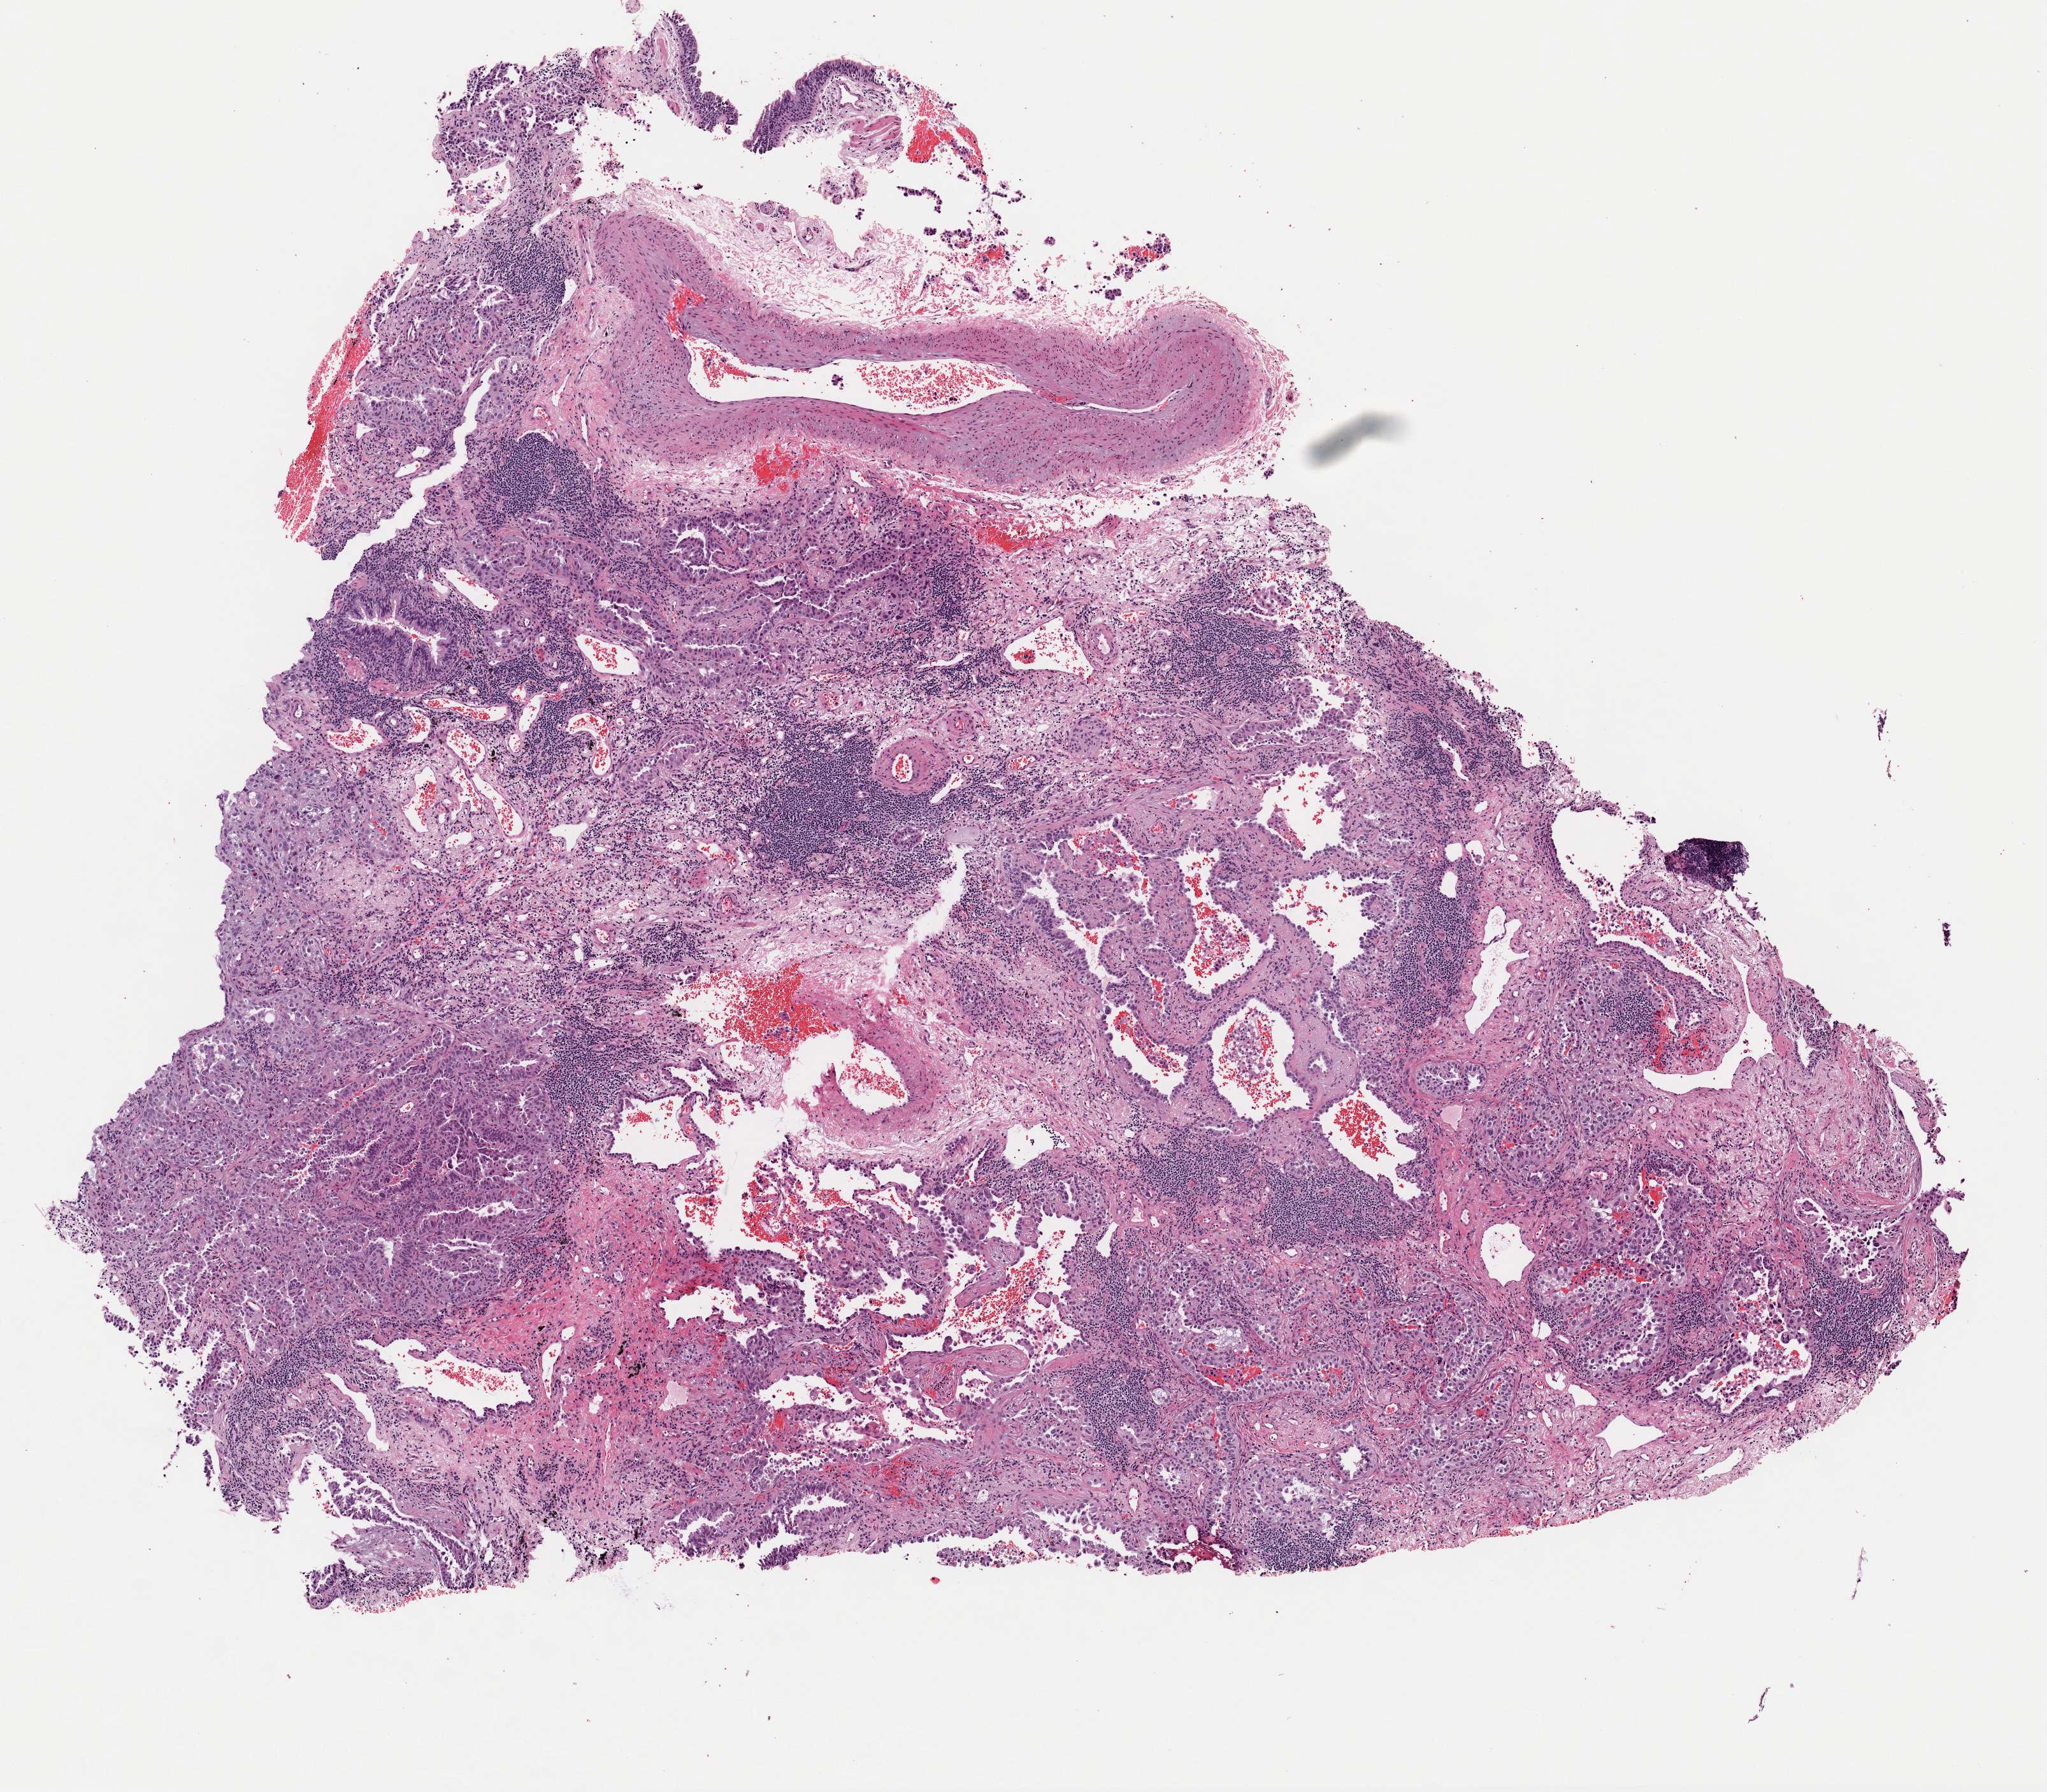
H&E whole-slide image, low-resolution overview of the scanned area, about 6.3 x 5.6 mm; frozen section; sample: primary tumour, lung. Female patient; age at initial diagnosis 67 years. Slide review estimates, as recorded: tumour cells 60%, tumour nuclei 80%, normal cells 5%, stromal cells 35%, necrosis 0%. Infiltration values recorded for this section: lymphocyte infiltration 20%, monocyte infiltration 2%, neutrophil infiltration 0%.
- AJCC pathologic stage: IA (7th edition)
- diagnosis: Adenocarcinoma, NOS (upper lobe, lung)